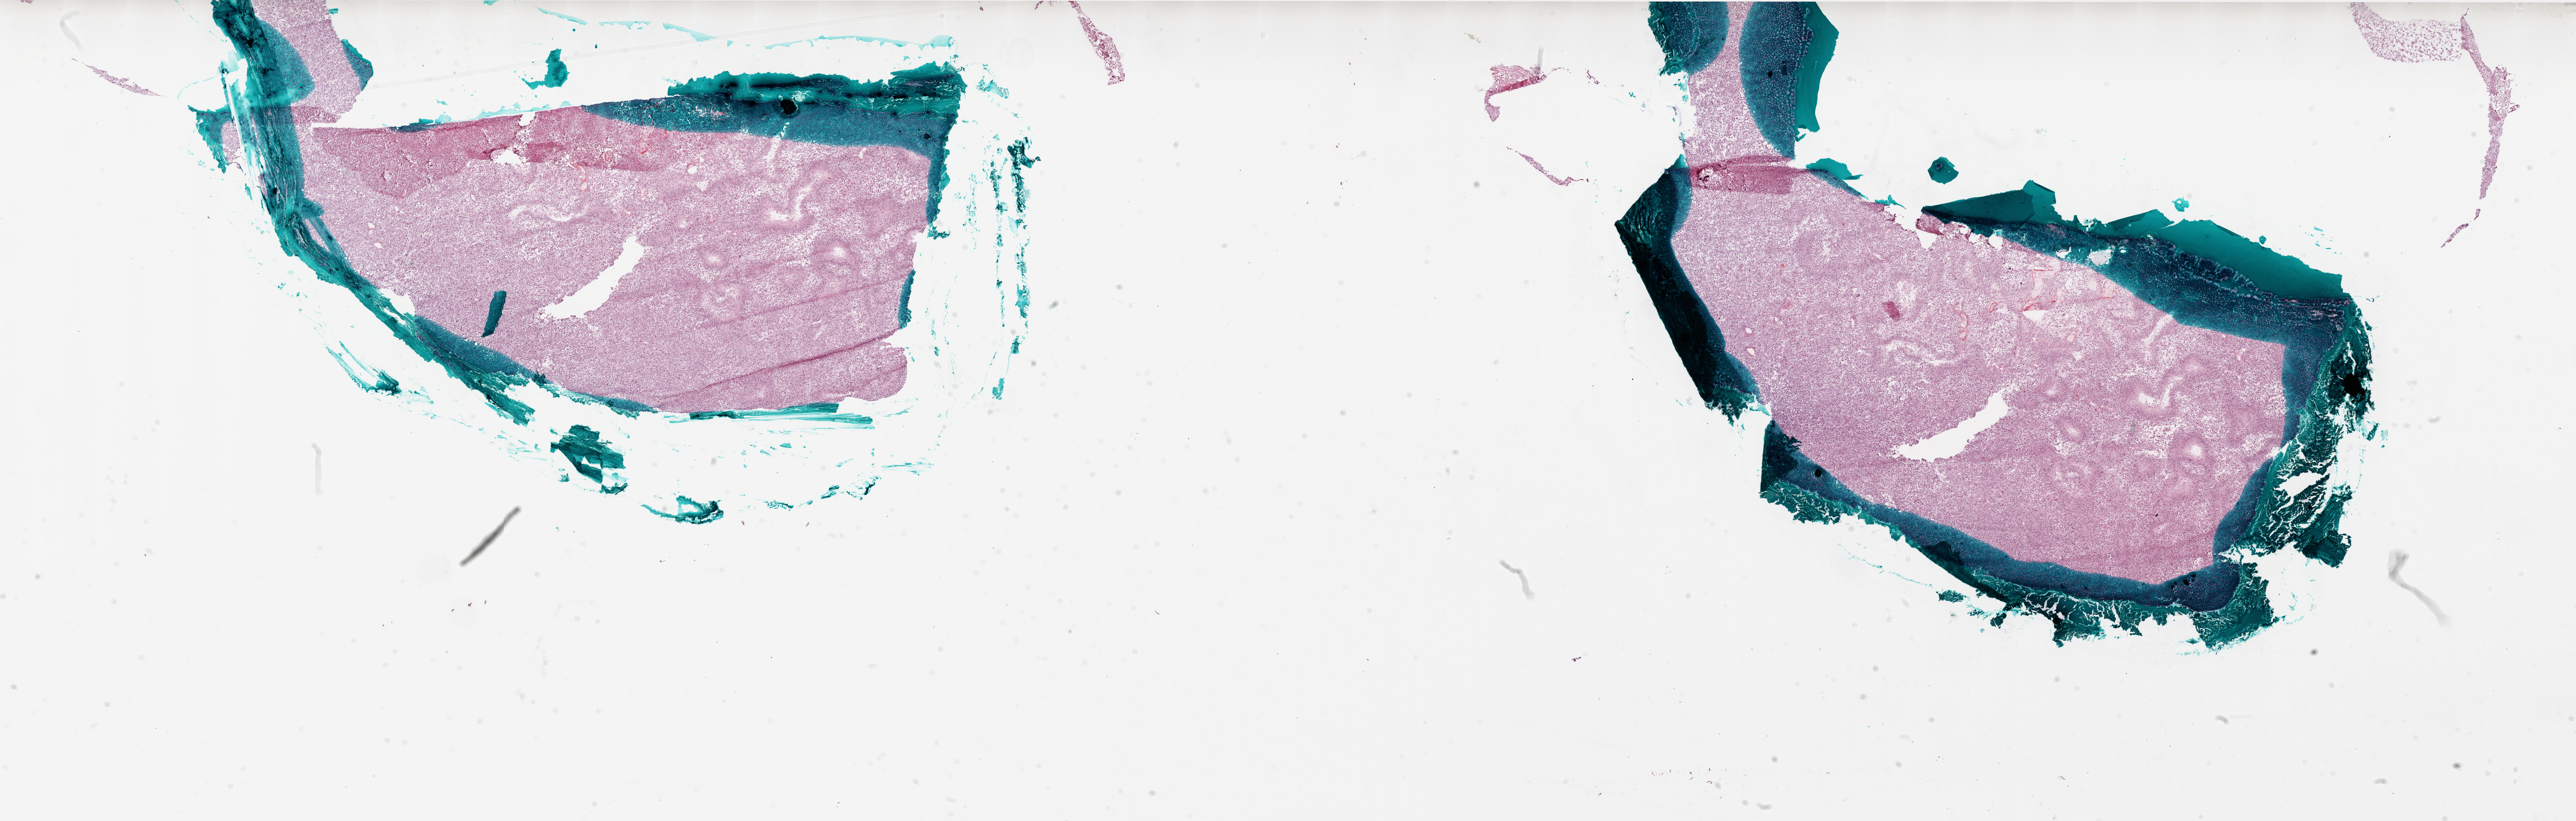
H&E-stained whole-slide image — whole scanned area (about 41.0 x 13.1 mm, from a 20x scan) shown as a low-resolution overview, frozen section from the bottom of the tissue portion, brain, primary tumour sample. Female patient; age at initial diagnosis 59 years. Pathologist review of this section (percent, as recorded): tumour cells 80%, tumour nuclei 100%, normal cells 0%, stromal cells 0%, necrosis 20%.
• diagnosis: Glioblastoma